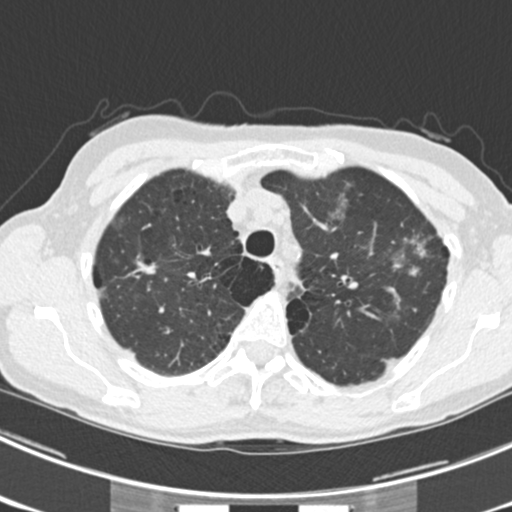
Low-dose screening chest CT, one axial slice. Position 174 of 225 along the scan axis. Reconstruction kernel B30f. 120 kVp. Lung window (W 1500 / L -600 HU). 2 mm slice thickness. 512 × 512 image matrix.
Structures marked on this image (outlined manually by an expert reader):
- lesion 1 (tumor, upper lobe of left lung): bounding box [x1, y1, x2, y2] px = [408, 266, 418, 277]
- lesion 5 (tumor, upper lobe of right lung): [133, 256, 161, 276]